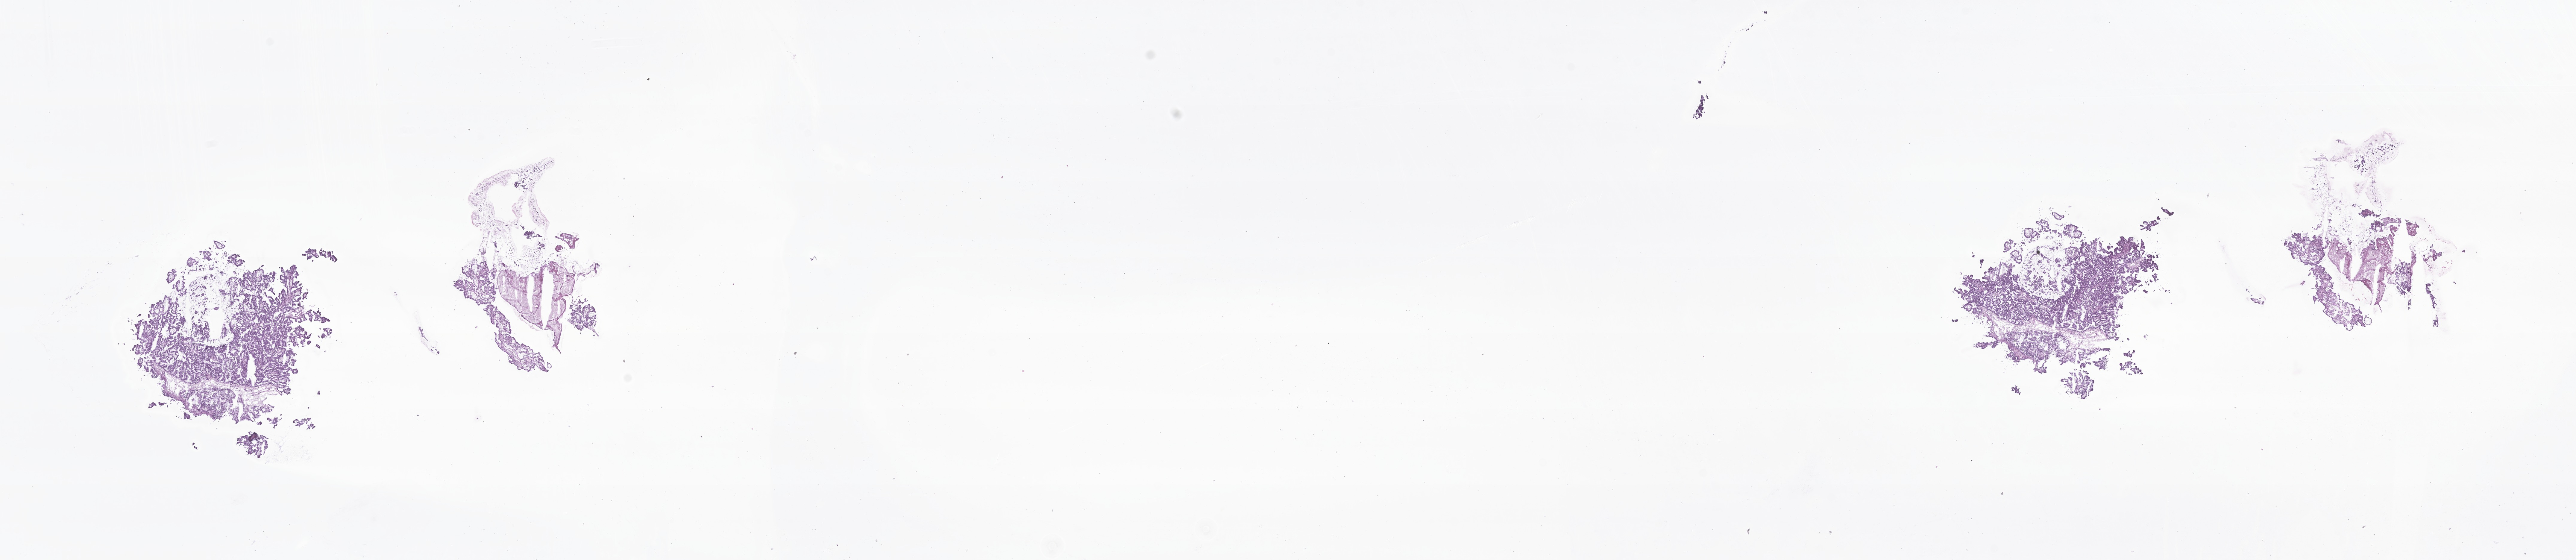
Whole-slide image, H&E stain of tumor tissue from the brain, low-resolution overview of the scanned area, about 36.3 x 7.9 mm. Frozen section. Male patient, age 166 days.
• diagnosis (ICD-O-3 morphology term): Atypical choroid plexus papilloma